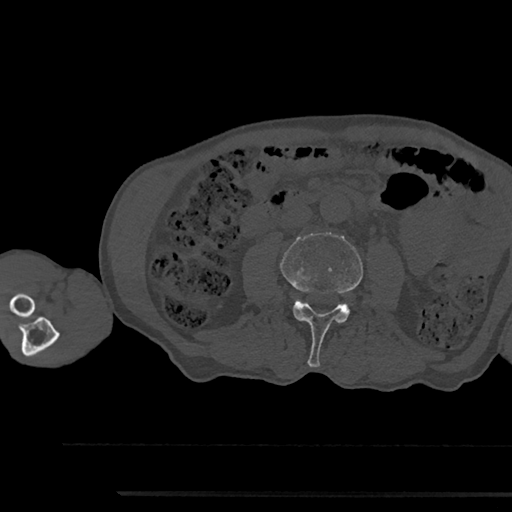
CT including the spine, one axial slice. Position 478 of 797 along the scan axis. Bone window (W 1800 / L 400 HU). 512 × 512 image matrix, field of view 367 × 367 mm. Male patient, age 79 years. Case-level facts recorded for this patient, not image findings: primary cancer: prostate.
Outlined on this slice (semi-automatic segmentation, software-assisted and operator-edited):
- L3 vertebra: box from (x=280, y=233) to (x=363, y=367) px